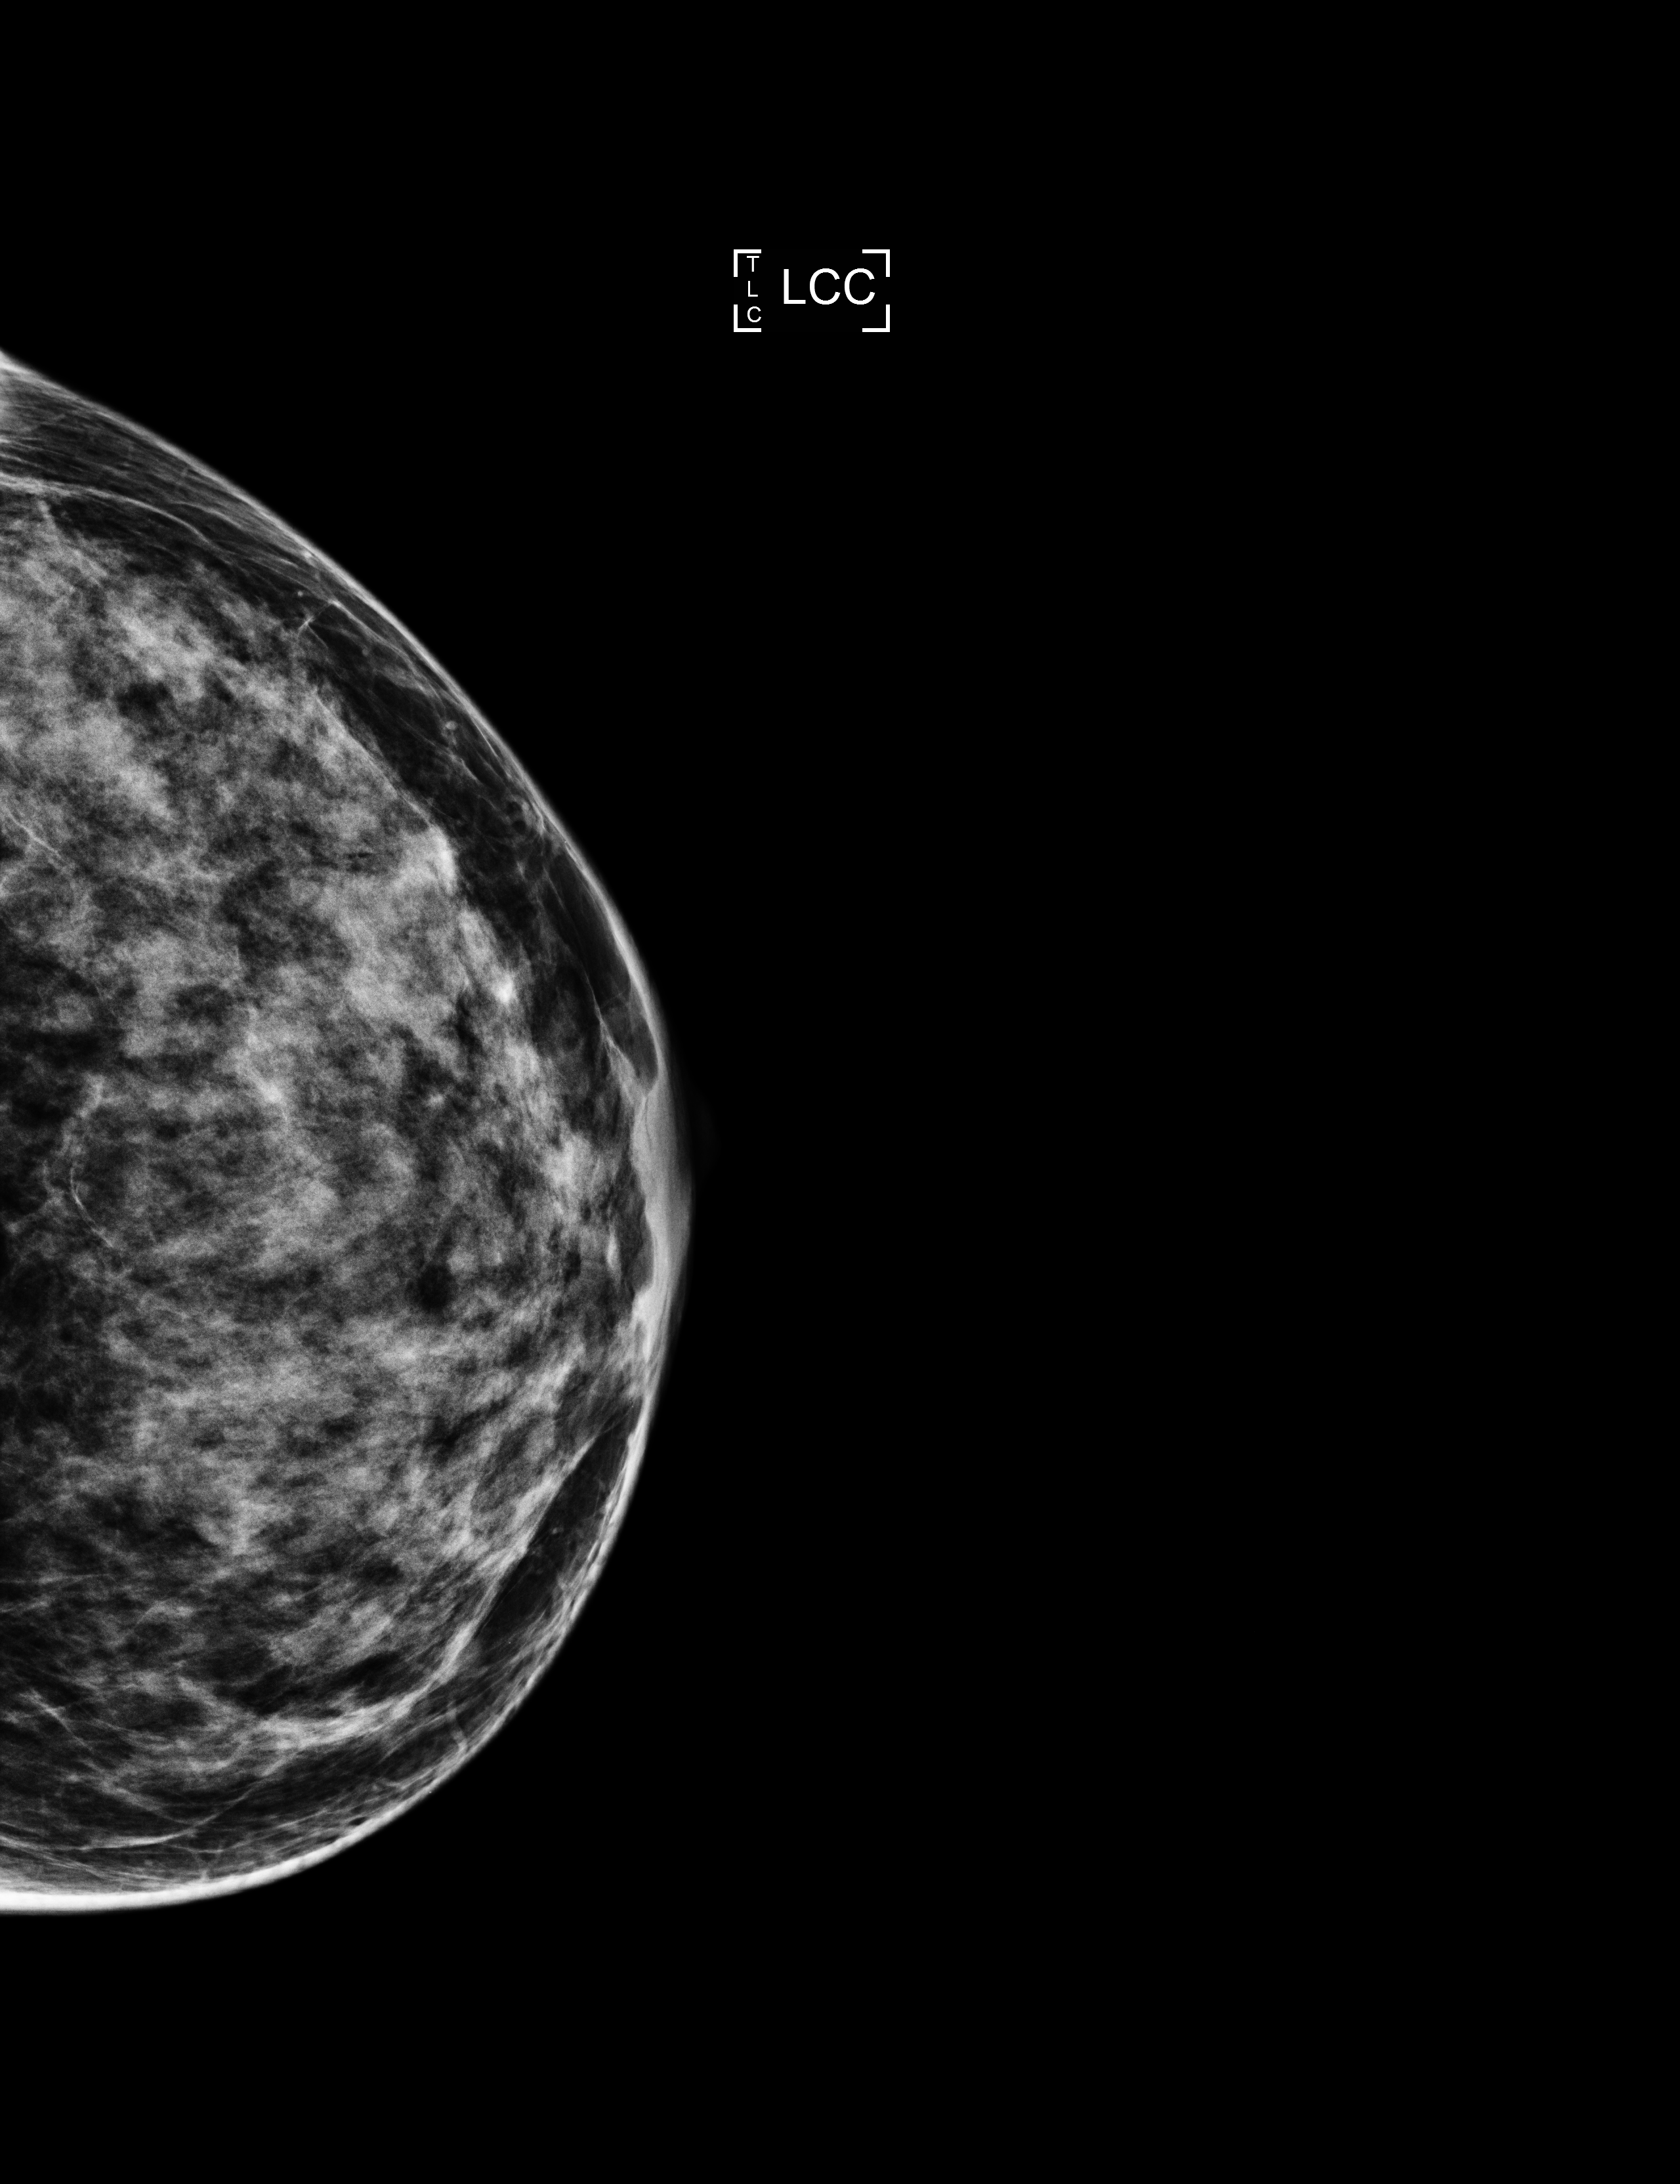
Screening examination, compressed breast thickness 47 mm. Female patient, age 53 years.
Image type: full-field digital mammogram. Breast: left. Projection: cranio-caudal projection.